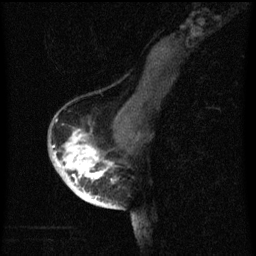
Breast MRI (dynamic contrast-enhanced), one sagittal slice. Position 39 of 60 along the scan axis. Dynamic contrast-enhanced series, image 2 of 3 at this slice position (ordered by acquisition). 1.5 T. TE 4.2 ms, TR 8 ms. 256 × 256 image matrix, field of view 180 × 180 mm. Patient: female, 56 years.
Annotated regions visible in this slice (semi-automatic segmentation, software-assisted and operator-edited):
- analysis volume of interest (the breast-tissue region the enhancement analysis was run in; not a lesion): box from (x=54, y=122) to (x=120, y=199) px
- tumour enhancement mask (voxels above the 70 % enhancement threshold inside the analysis volume of interest): (x=54, y=130)–(x=114, y=199)